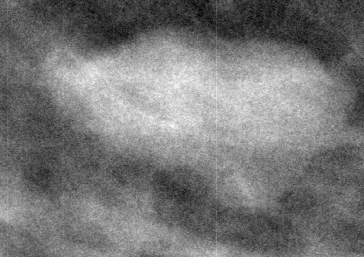
Crop from a digitized film mammogram around one marked abnormality, left breast, MLO view.
Finding: mass, shape oval, margins circumscribed; BI-RADS assessment category 2; subtlety rating 5 on a 1 (subtle) to 5 (obvious) scale; pathology result (as recorded, not read from the image): benign.